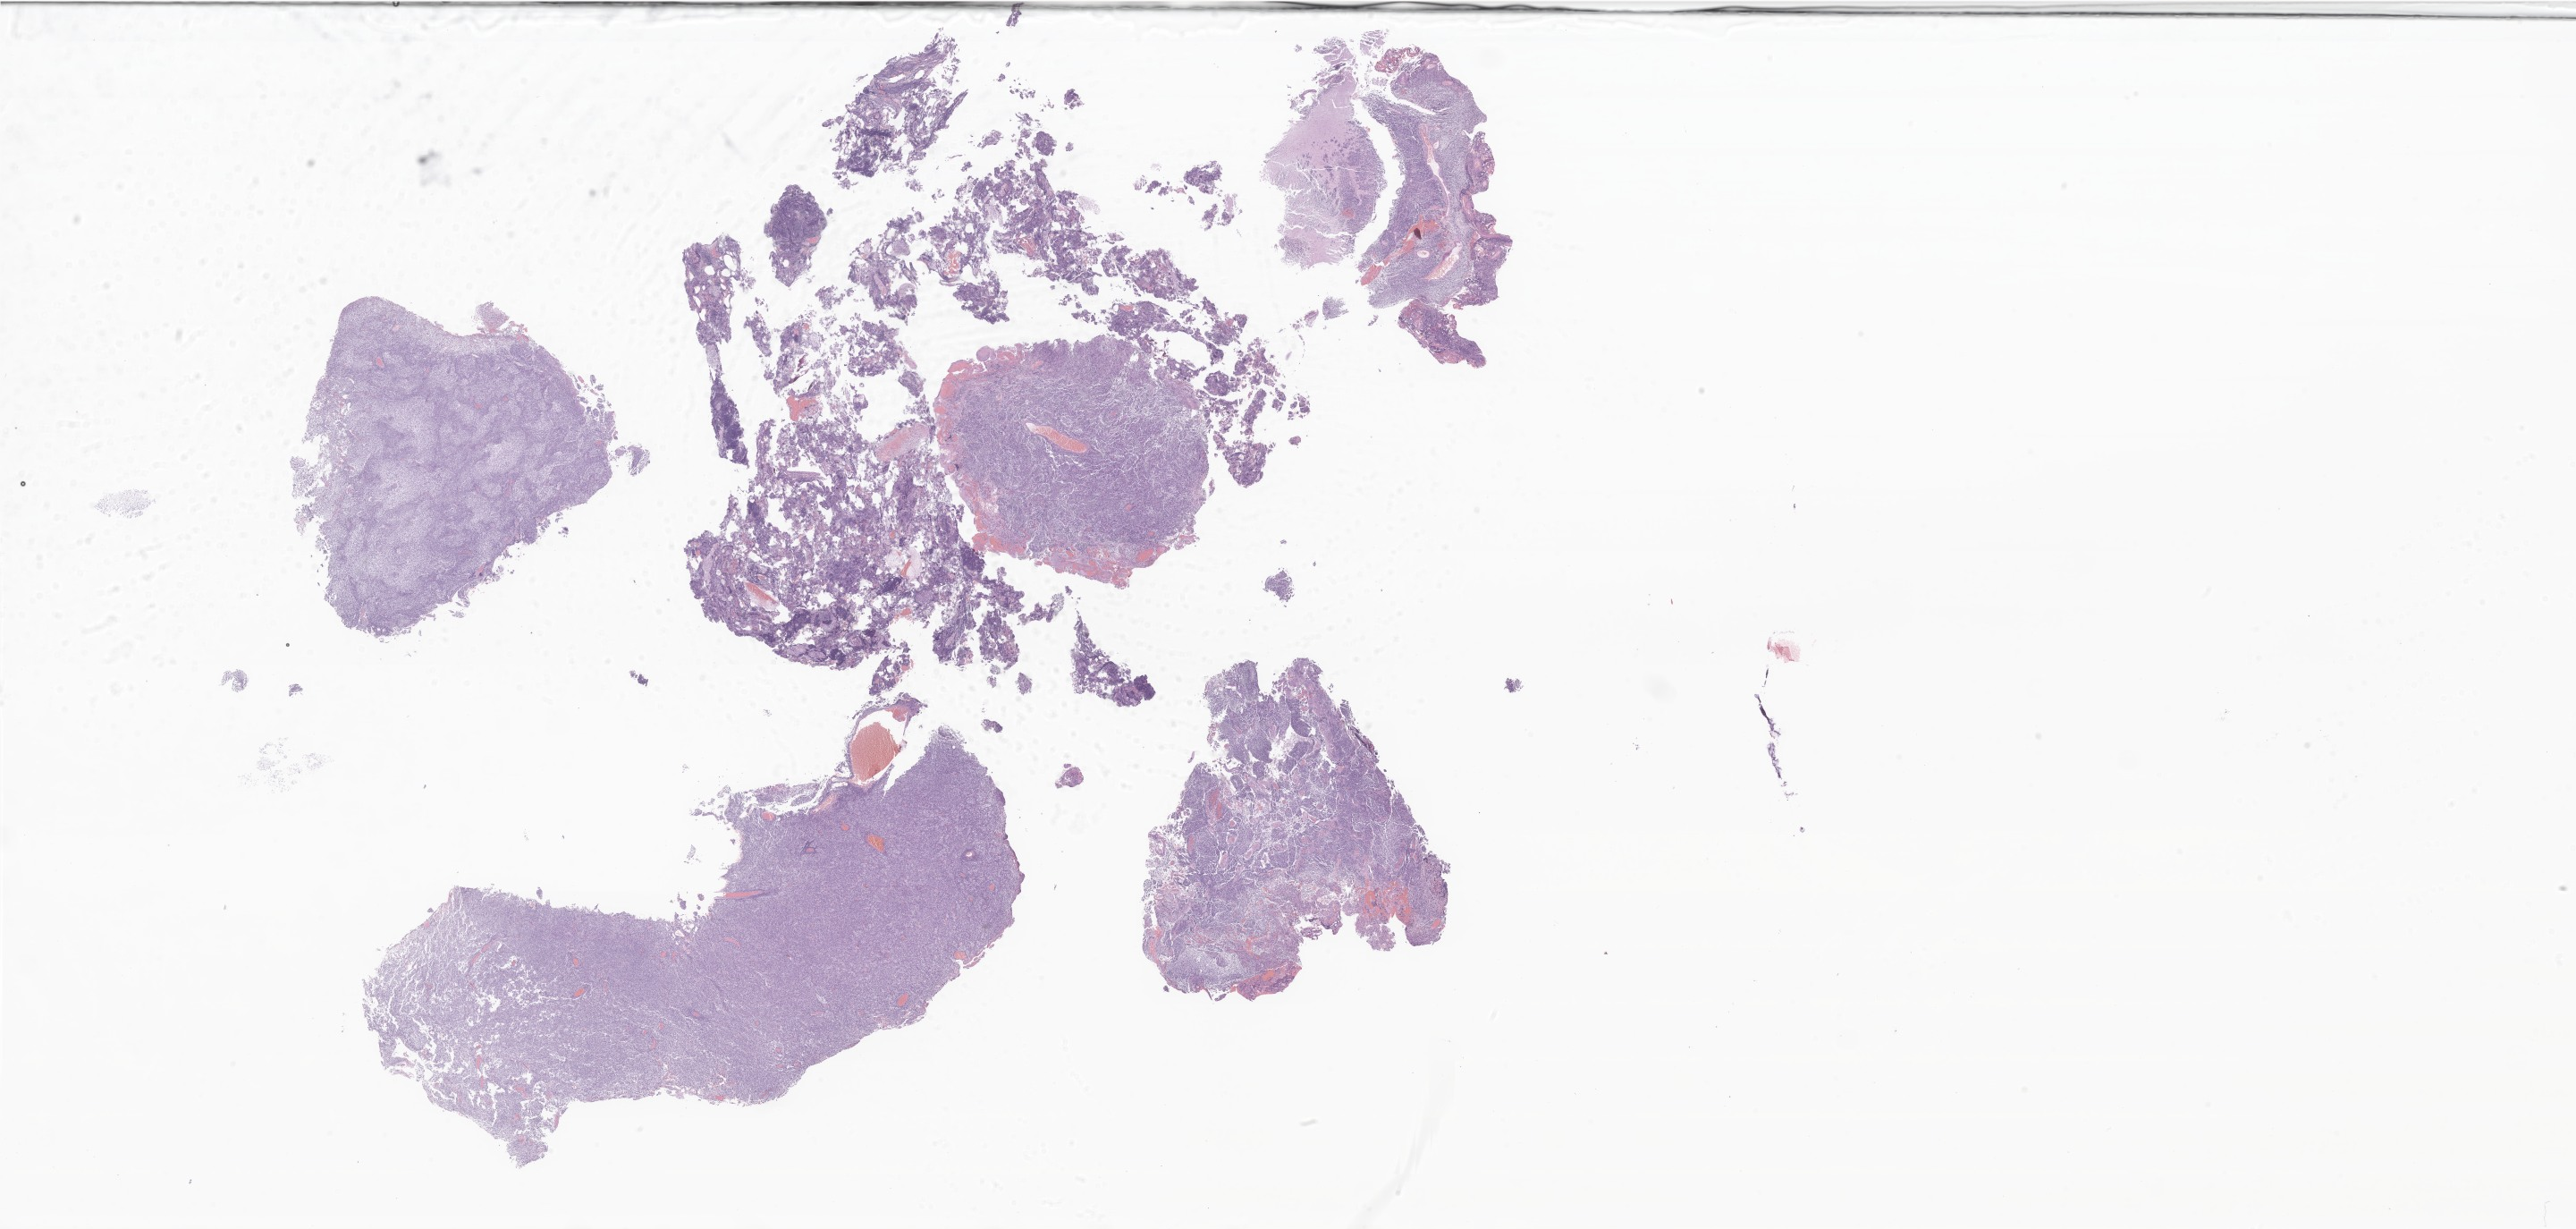
Whole-slide image, H&E stain of tumor tissue from the cerebellum, a low-resolution overview of the entire scanned area, about 48.6 x 23.2 mm; formalin-fixed, paraffin-embedded (FFPE) tissue. Patient: male, age 164 months (13 years 8 months).
Recorded diagnosis: Medulloblastoma, NOS.